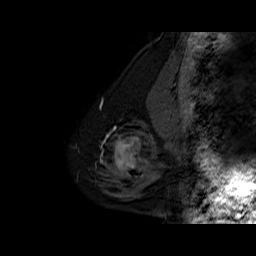
Breast MRI (dynamic contrast-enhanced), one sagittal slice. Position 14 of 60 along the scan axis. Dynamic contrast-enhanced series, time point 2 of 6 at this slice position (early post-contrast). 1.5 T. TE 6.3 ms, TR 32.5 ms. 4 mm slice thickness. 256 × 256 image matrix, field of view 200 × 200 mm. Female patient. From the clinical record (not read from this slice): setting: breast cancer imaged before/during neoadjuvant chemotherapy; receptor status: triple-negative.
Structures marked on this image (semi-automatically segmented with operator editing):
- analysis volume of interest (the breast-tissue region the enhancement analysis was run in; not a lesion): bounding box (x1, y1, x2, y2) in pixels: (102, 127, 162, 186)
- tumour enhancement mask (voxels above the 100 % enhancement threshold inside the analysis volume of interest): (114, 136, 152, 172)